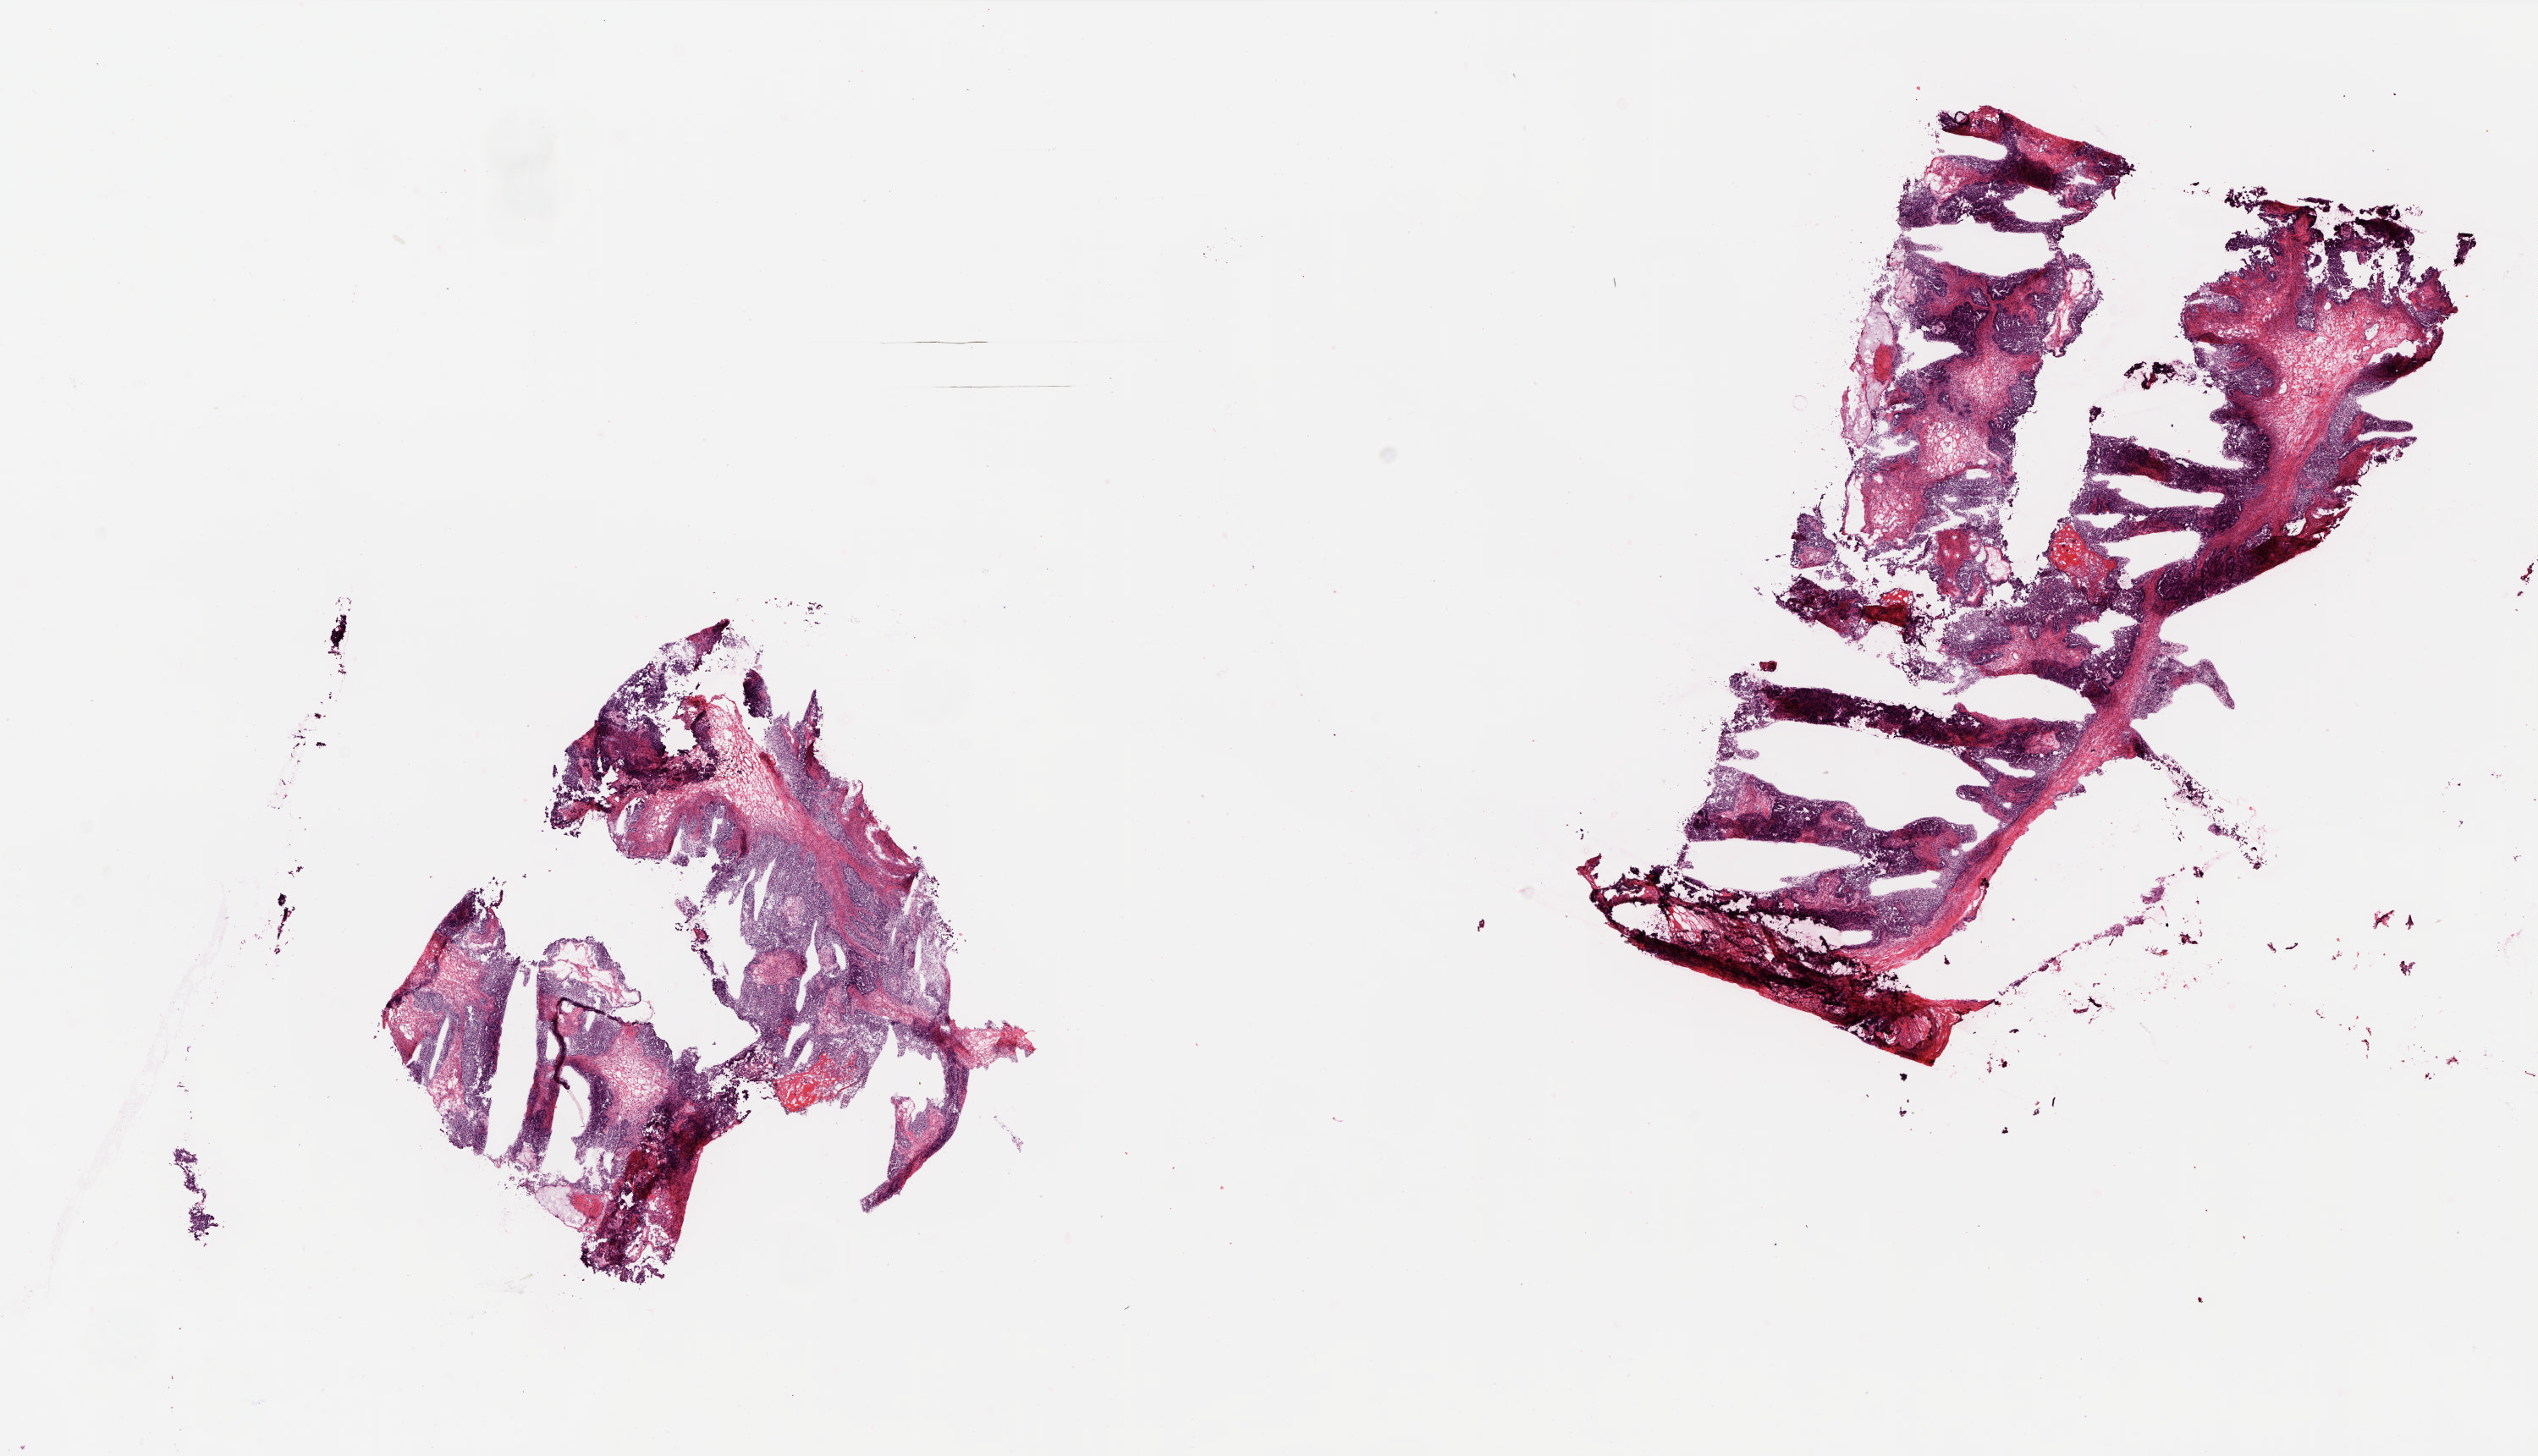
Hematoxylin and eosin (H&E) stained whole-slide image, low-resolution overview of the scanned area, about 24.0 x 13.7 mm; frozen section; ovary, primary tumour sample. Female patient; age at initial diagnosis 52 years. Histologic grade: G2 (moderately differentiated). Composition of this section per pathologist review: tumour cells 79%, tumour nuclei 80%, normal cells 0%, stromal cells 20%, necrosis 1%.
* diagnosis: Serous cystadenocarcinoma, NOS
* laterality: bilateral
* FIGO stage: IIIB